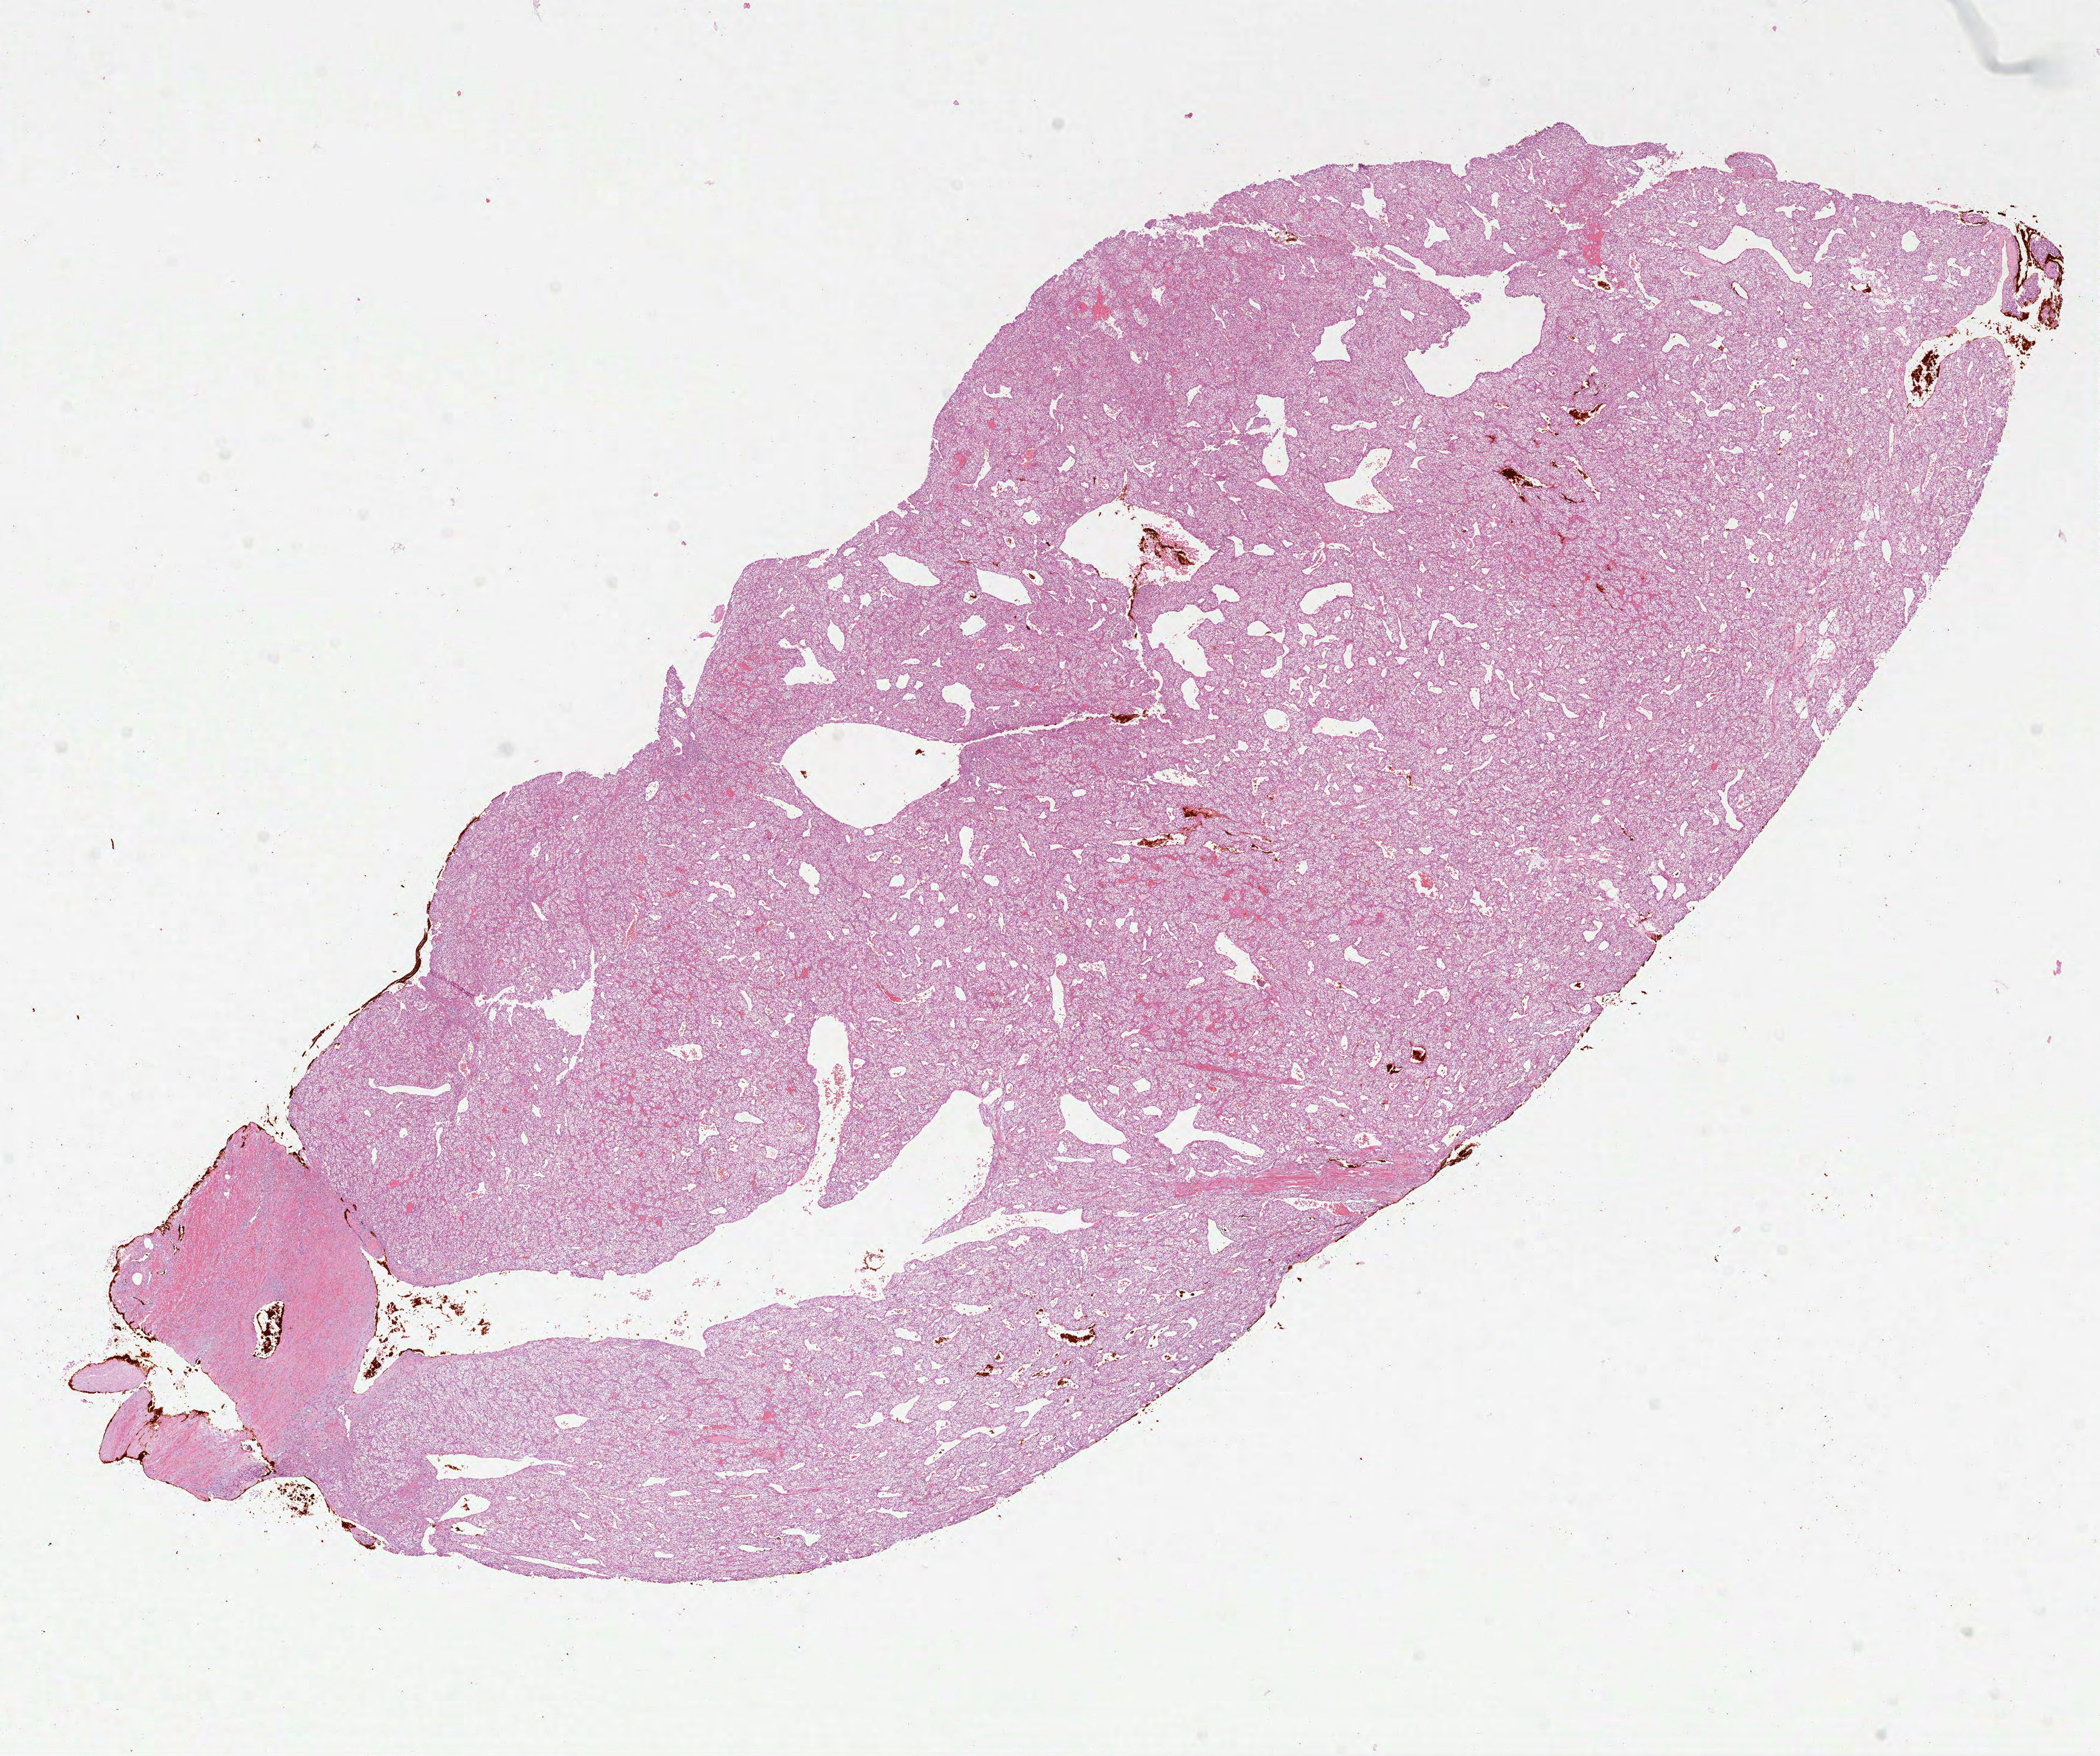
Digitized H&E-stained tissue section (whole slide) — a low-resolution overview of the entire scanned area, about 14.0 x 11.7 mm (acquisition: 40x scan); formalin-fixed paraffin-embedded (FFPE) diagnostic section; kidney, primary tumour sample. Male patient; age at initial diagnosis 42 years. Histologic grade: G2 (moderately differentiated).
- AJCC pathologic stage: II
- pathologic diagnosis: Clear cell adenocarcinoma, NOS
- laterality: right